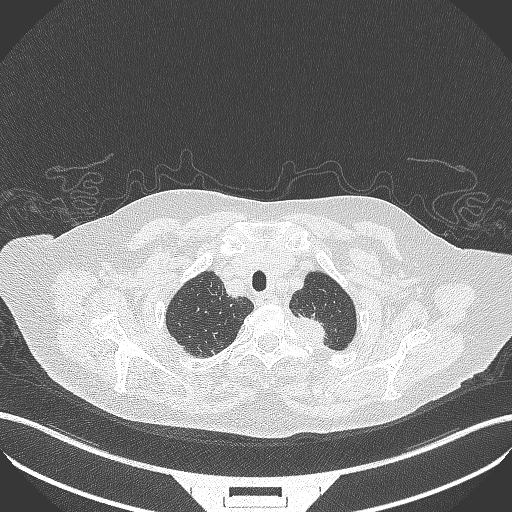
Chest CT, one axial slice. Slice 306 of 353 in the series (ordered by position). 100 kVp. Lung window (W 1500 / L -600 HU). 512 × 512 image matrix. Patient: female, 81 years. Case-level facts recorded for this patient, not image findings: clinical TNM (as recorded): T2a N0 M0.
Outlined on this slice (bounding box drawn by a radiologist):
- lung tumour (recorded histology: adenocarcinoma): bounding box (x1, y1, x2, y2) in pixels: (285, 309, 345, 354)